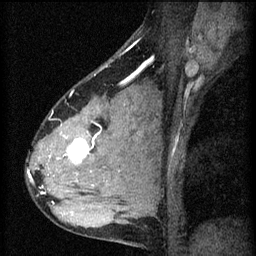
Breast MRI (dynamic contrast-enhanced), one sagittal slice; 3 images stored at this slice position (order not interpretable as contrast timing); 1.5 T; TE 4.2 ms, TR 8.2 ms; 256 × 256 image matrix, field of view 180 × 180 mm. Female patient, age 37 years.
Structures marked on this image (semi-automatic segmentation, software-assisted and operator-edited):
- analysis volume of interest (the breast-tissue region the enhancement analysis was run in; not a lesion): bounding box [x1, y1, x2, y2] px = [44, 100, 119, 197]
- tumour enhancement mask (voxels above the 70 % enhancement threshold inside the analysis volume of interest): [64, 132, 93, 163]